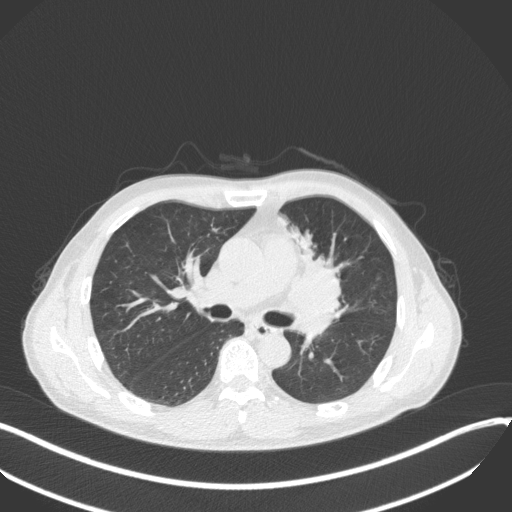
Chest CT, one axial slice; slice 199 of 411 in the series (ordered by position); reconstruction kernel B31f; lung window (W 1500 / L -600 HU); 512 × 512 image matrix, field of view 400 × 400 mm. Male patient, age 56 years. Case-level facts recorded for this patient, not image findings: clinical TNM (as recorded): T2a N0 M0.
Outlined on this slice (bounding box drawn by a radiologist):
- lung tumour (recorded histology: squamous cell carcinoma): bounding box (x1, y1, x2, y2) in pixels: (290, 228, 351, 322)